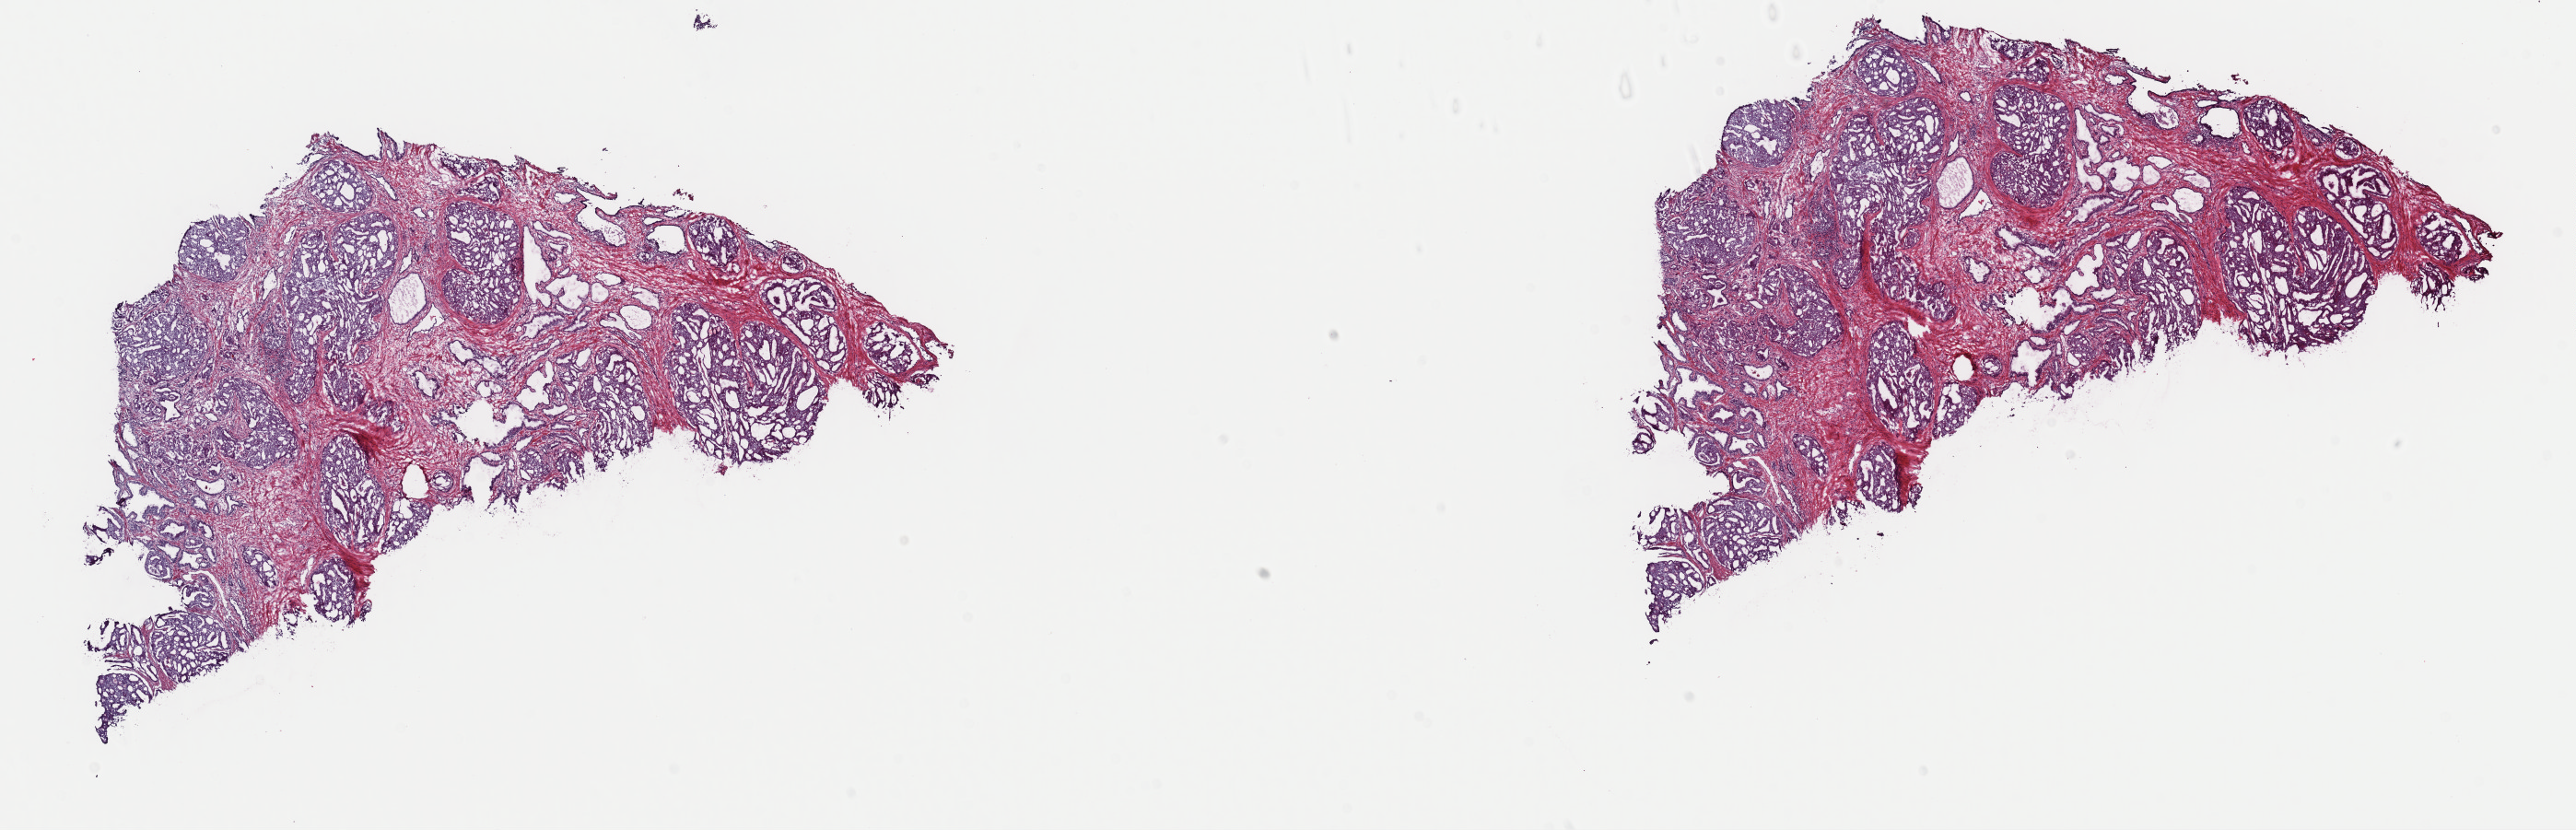
H&E-stained whole-slide image, shown as a low-resolution overview of the whole scanned area (about 22.1 x 7.1 mm). Frozen section from the top of the tissue portion. Primary tumour sample from the prostate. Patient: male, age at initial diagnosis 59 years. Gleason score: 9 (4+5). Composition of this section per pathologist review: tumour cells 70%, tumour nuclei 70%, normal cells 0%, stromal cells 30%, necrosis 0%. Inflammatory infiltration, as recorded: lymphocyte infiltration 40%, monocyte infiltration 20%, neutrophil infiltration 20%.
* pathologic diagnosis: Adenocarcinoma, NOS (prostate gland)
* lymph nodes positive (case pathology): 0 of 9 examined